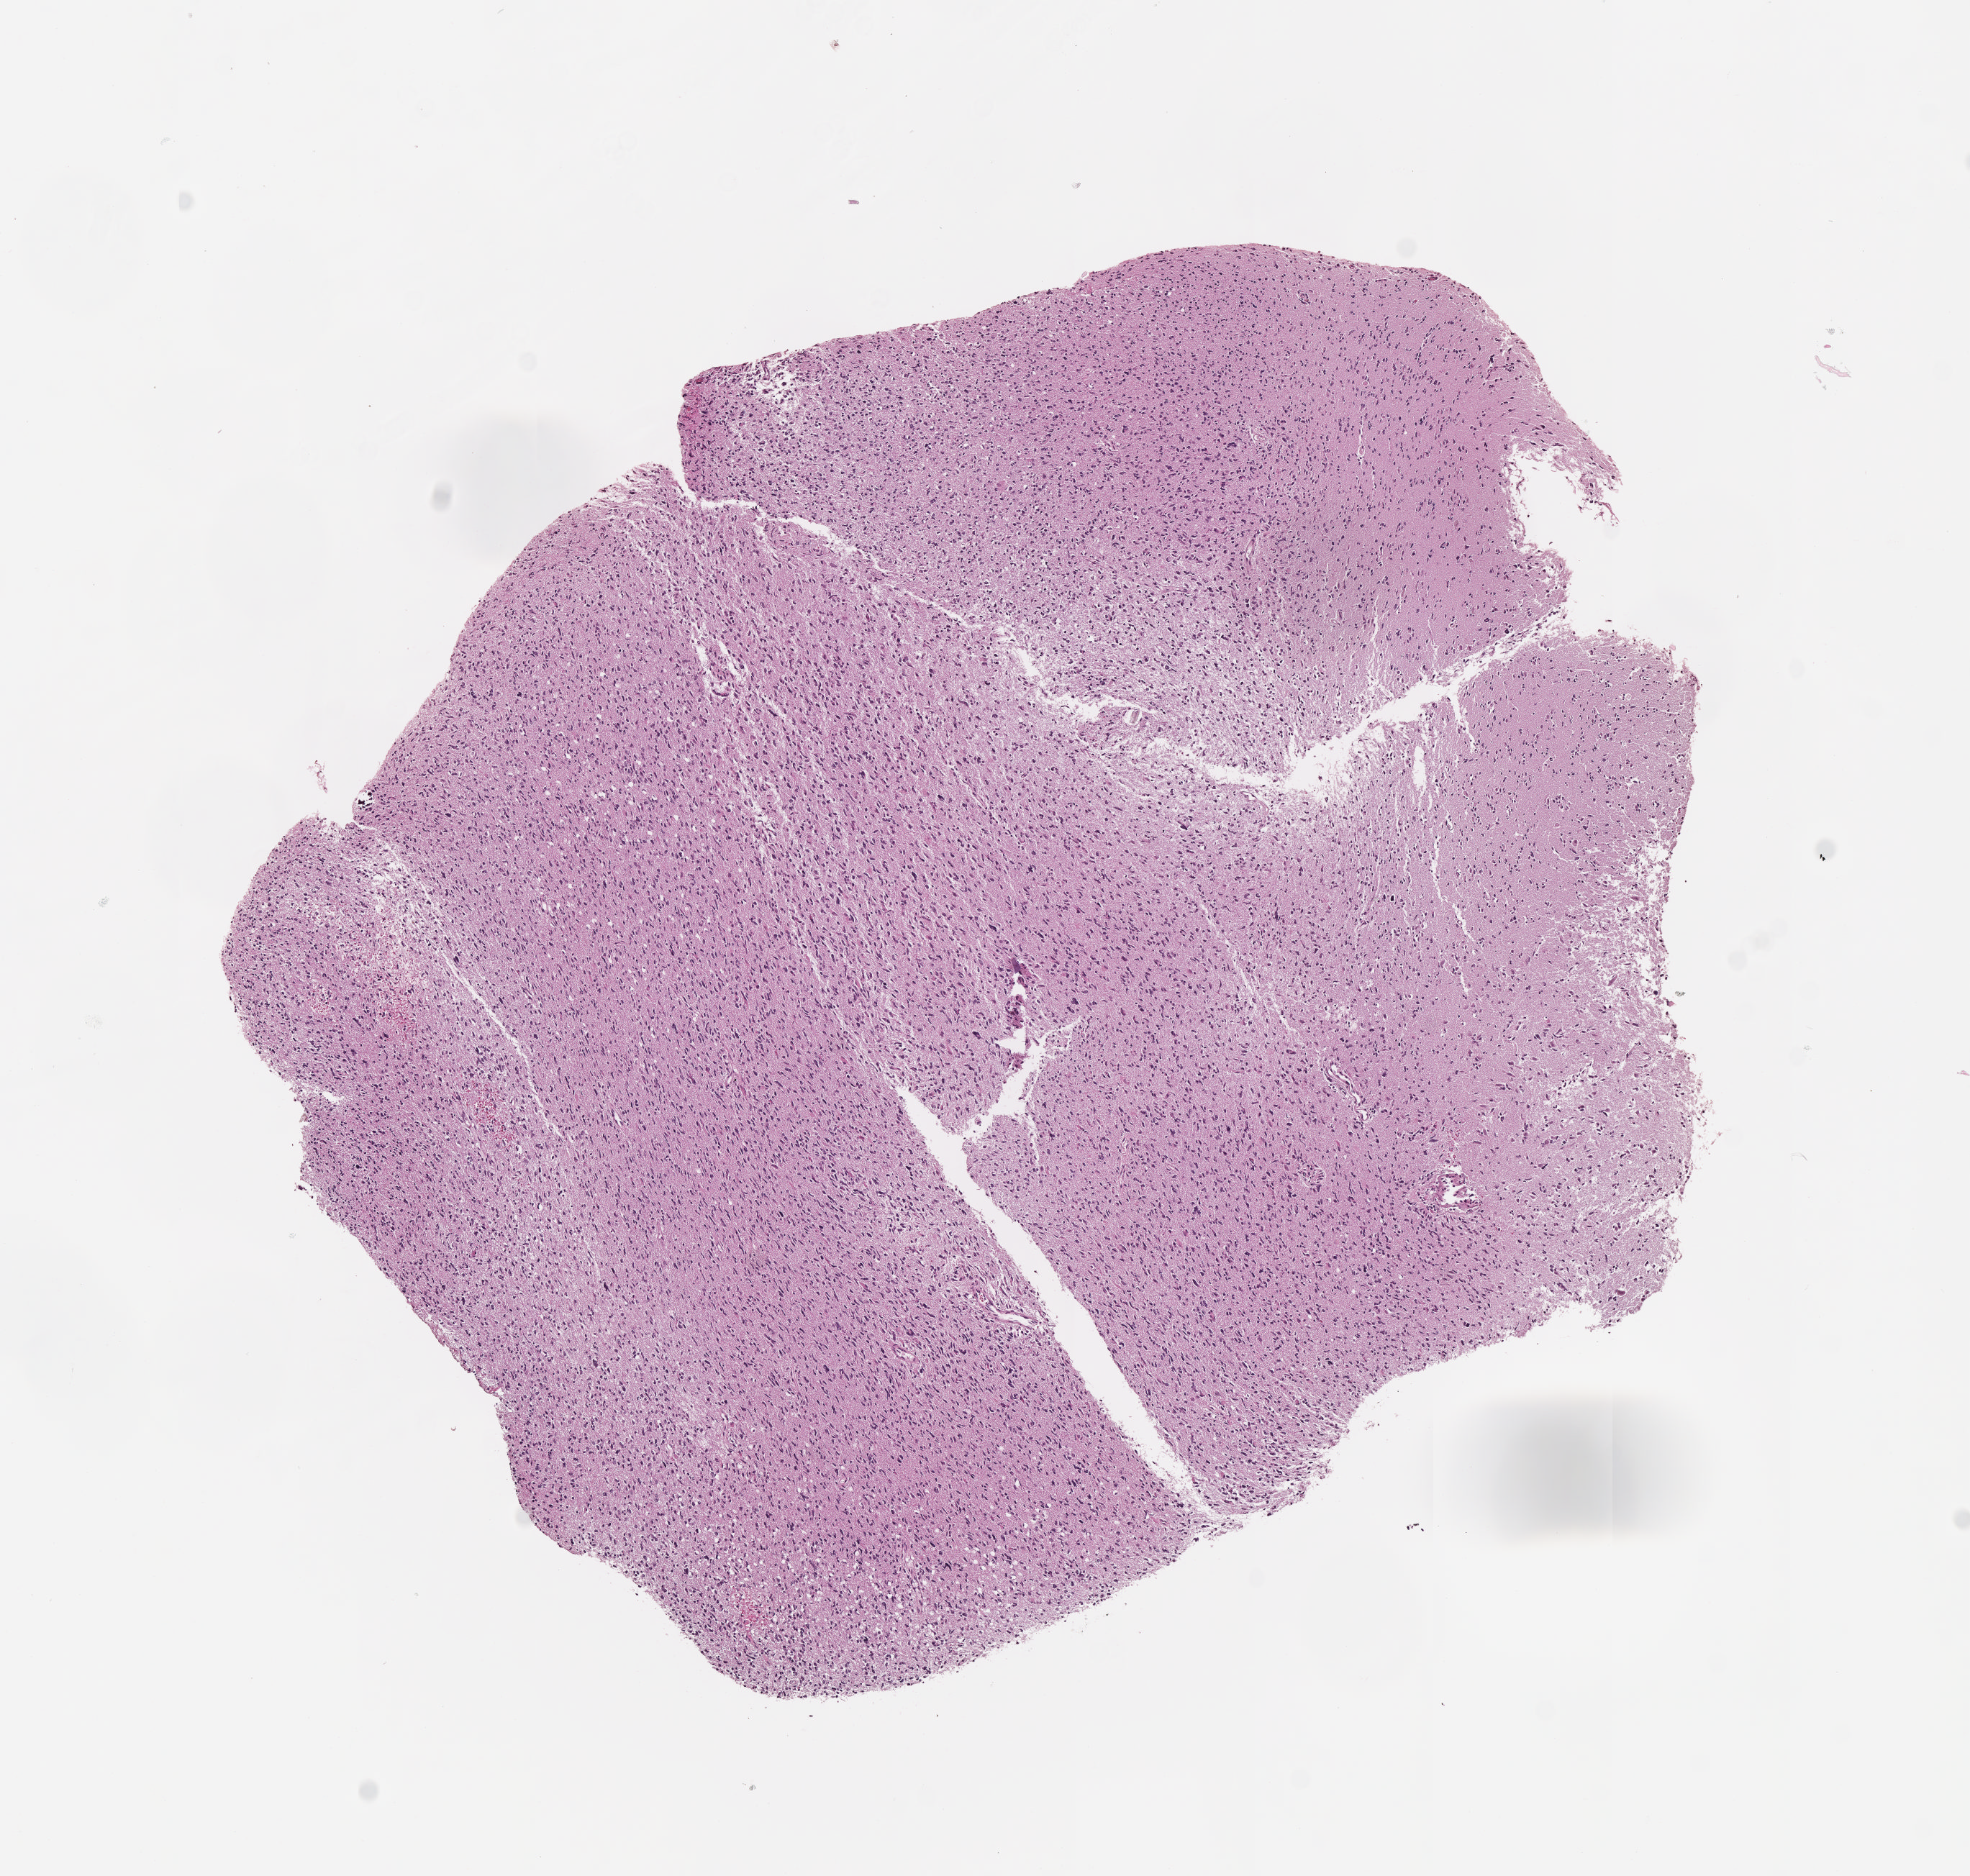
Hematoxylin and eosin (H&E) stained whole-slide image, whole scanned area (about 5.5 x 5.3 mm, slide scanned at 40x) shown as a low-resolution overview. FFPE section. Sample: primary tumour, brain. Patient: male, age at initial diagnosis 33 years.
Histologic diagnosis: Astrocytoma, anaplastic.